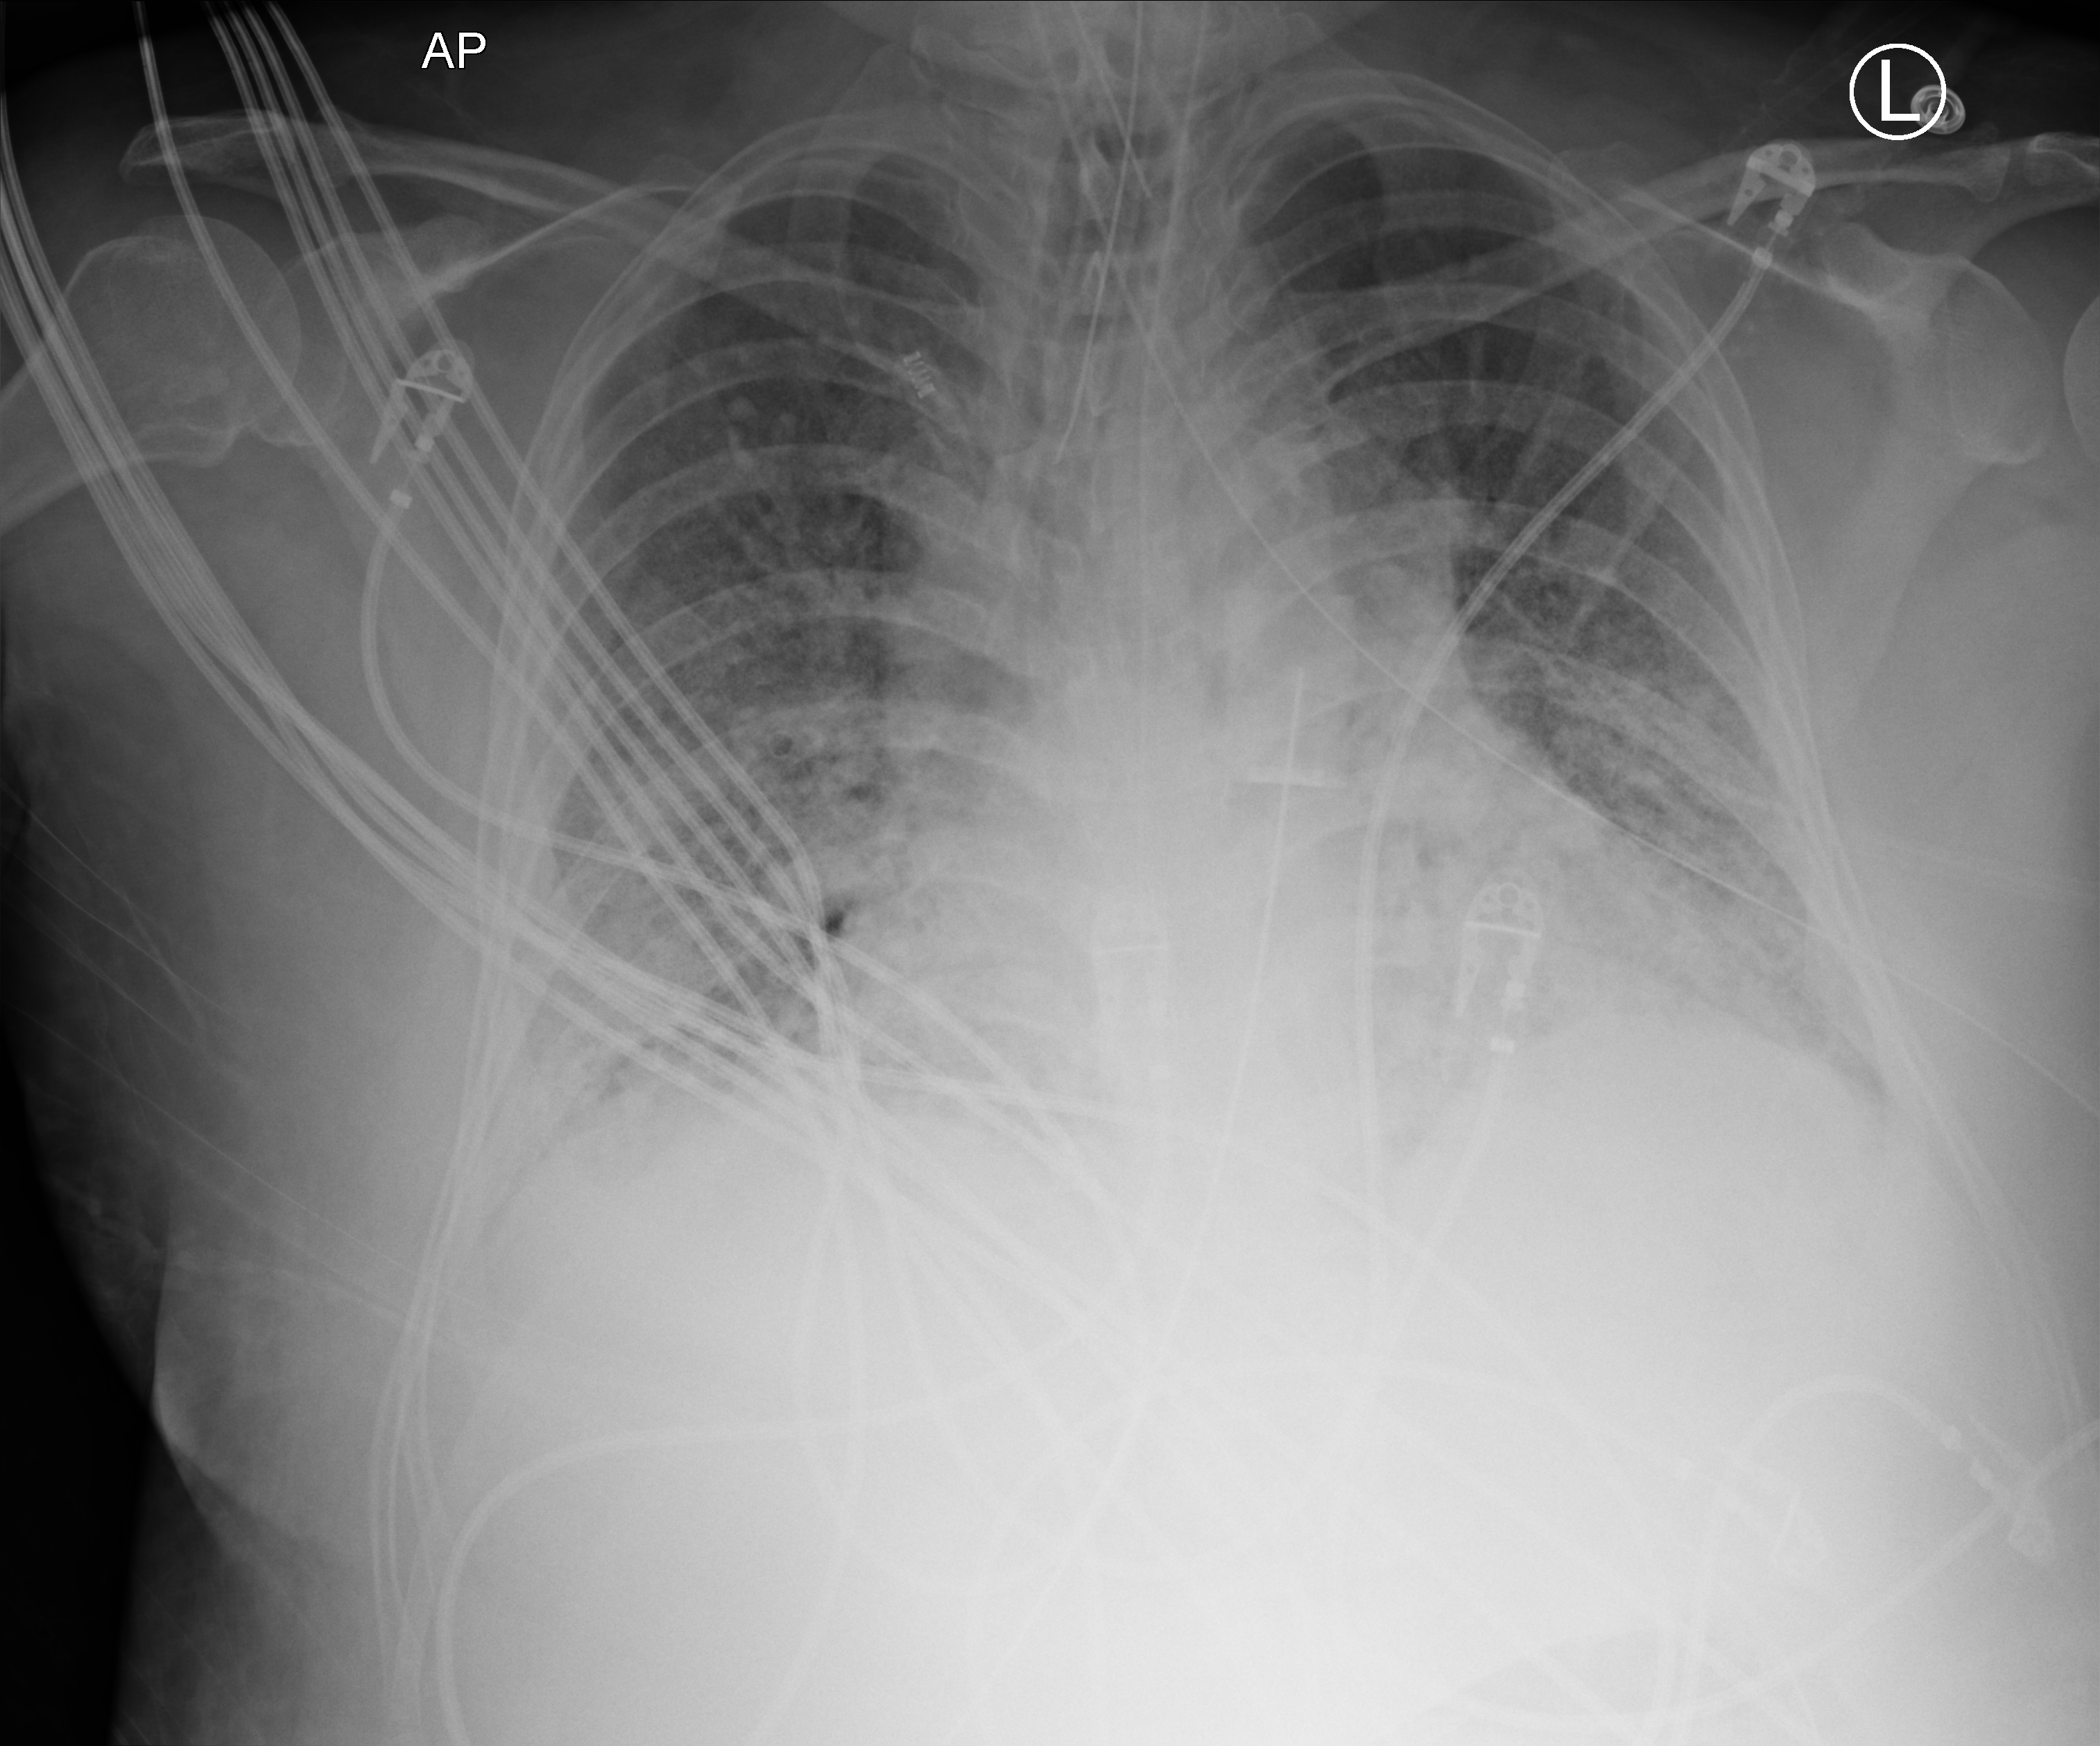
Chest X-ray (portable), anteroposterior (AP) projection. Patient hospitalised with COVID-19, aged 18–59 years.
Hospital-stay facts (about this admission, not read from this image; timing relative to this image not recorded): smoking status (admission record): never; mechanically ventilated during this hospital stay: yes; admitted to intensive care during this hospital stay: yes.